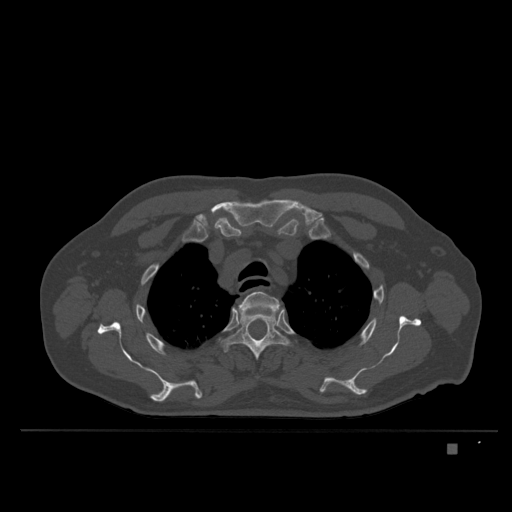
CT including the spine, one axial slice. Position 291 of 435 along the scan axis. Bone window (W 1800 / L 400 HU). 1.5 mm slice thickness. 512 × 512 image matrix, field of view 434 × 434 mm. Patient: male, 73 years. Case-level facts recorded for this patient, not image findings: primary cancer: skin.
Structures marked on this image (semi-automatic segmentation, software-assisted and operator-edited):
- T3 vertebra: bounding box (x1, y1, x2, y2) in pixels: (238, 291, 282, 311)
- T4 vertebra: (223, 312, 289, 360)